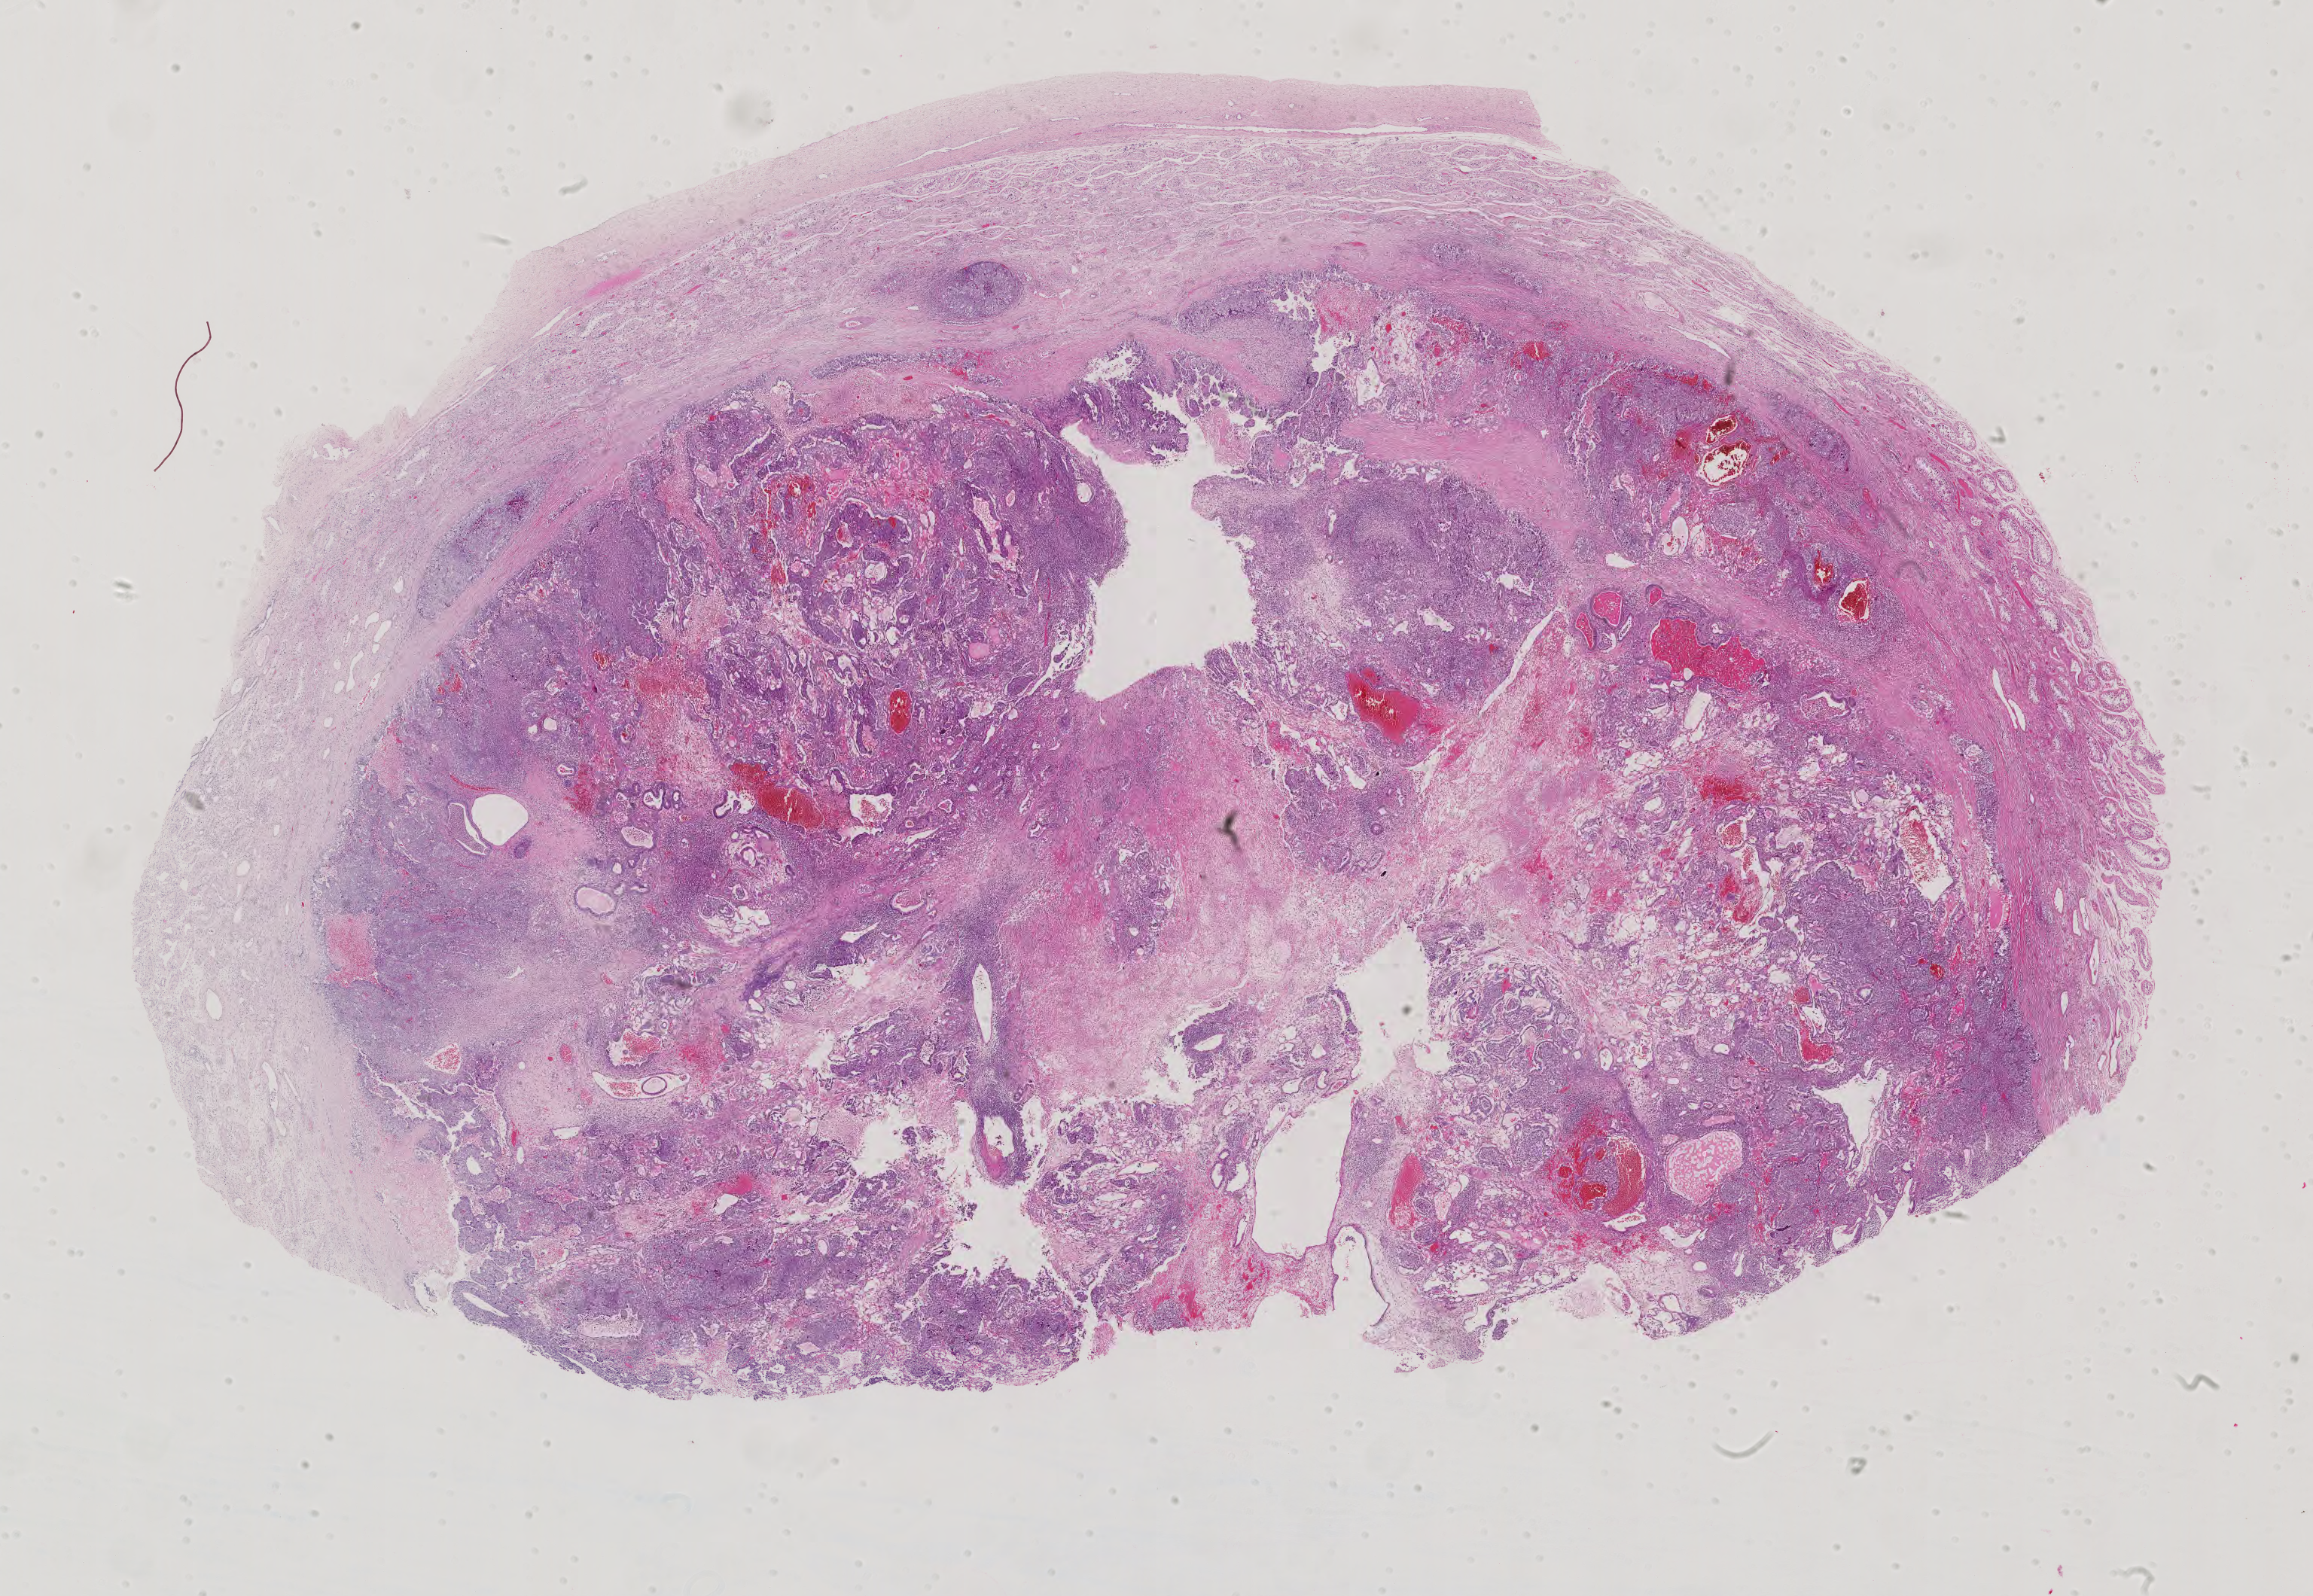
Hematoxylin and eosin (H&E) stained whole-slide image, low-resolution overview of the scanned area, about 22.4 x 15.4 mm. FFPE section. Sample: primary tumour, testis. Patient: male, age at initial diagnosis 20 years.
- pathologic diagnosis: Mixed germ cell tumor
- AJCC pathologic stage: IS (6th edition)